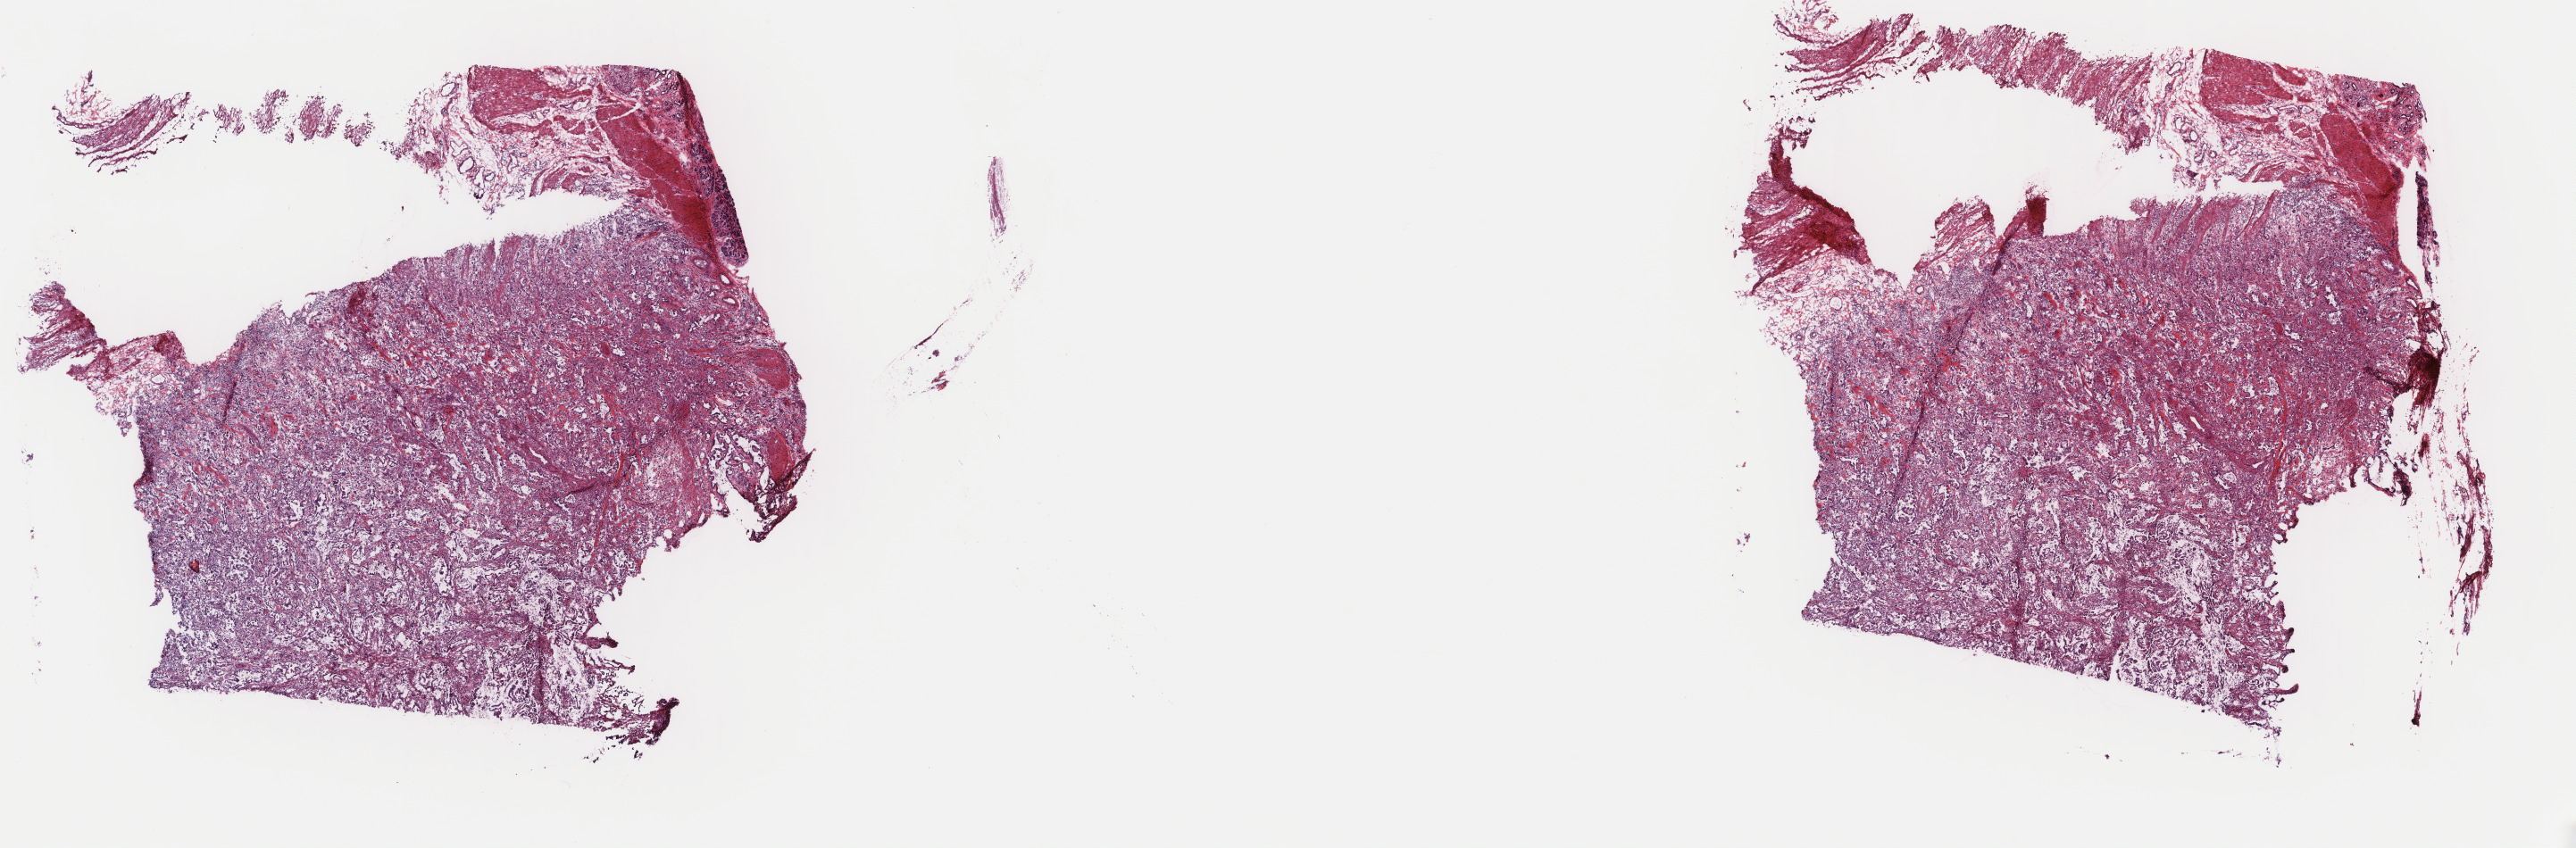
Digitized H&E tissue section (whole slide), whole scanned area (about 22.9 x 7.5 mm, acquisition: 40x scan) shown as a low-resolution overview. Frozen section from the top of the tissue portion. Primary tumour sample from the pancreas. Patient: male, age at initial diagnosis 48 years. Histologic grade: G2 (moderately differentiated). Pathologist review of this section (percent, as recorded): tumour cells 70%, tumour nuclei 80%, normal cells 0%, stromal cells 30%, necrosis 0%. Infiltration values recorded for this section: lymphocyte infiltration 0%, monocyte infiltration 0%, neutrophil infiltration 0%.
Pathologic diagnosis: Mucinous adenocarcinoma. AJCC pathologic stage: IIA (7th edition). TNM: T3 NX M0.